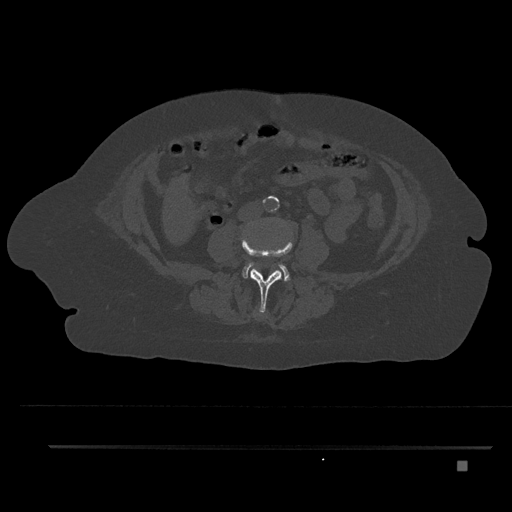
CT including the spine, one axial slice; position 113 of 797 along the scan axis; reconstruction kernel Br40s/3; bone window (W 1800 / L 400 HU); 0.5 mm slice thickness; 512 × 512 image matrix, field of view 437 × 437 mm. Female patient, age 76 years. From the clinical record (not read from this slice): primary cancer: lung; vertebrae with lytic lesions (as recorded): T11, L3.
Structures marked on this image (semi-automatically segmented with operator editing):
- L2 vertebra: bounding box [x1, y1, x2, y2] px = [259, 312, 263, 315]
- L3 vertebra: [242, 233, 293, 313]
- L4 vertebra: [242, 237, 290, 282]